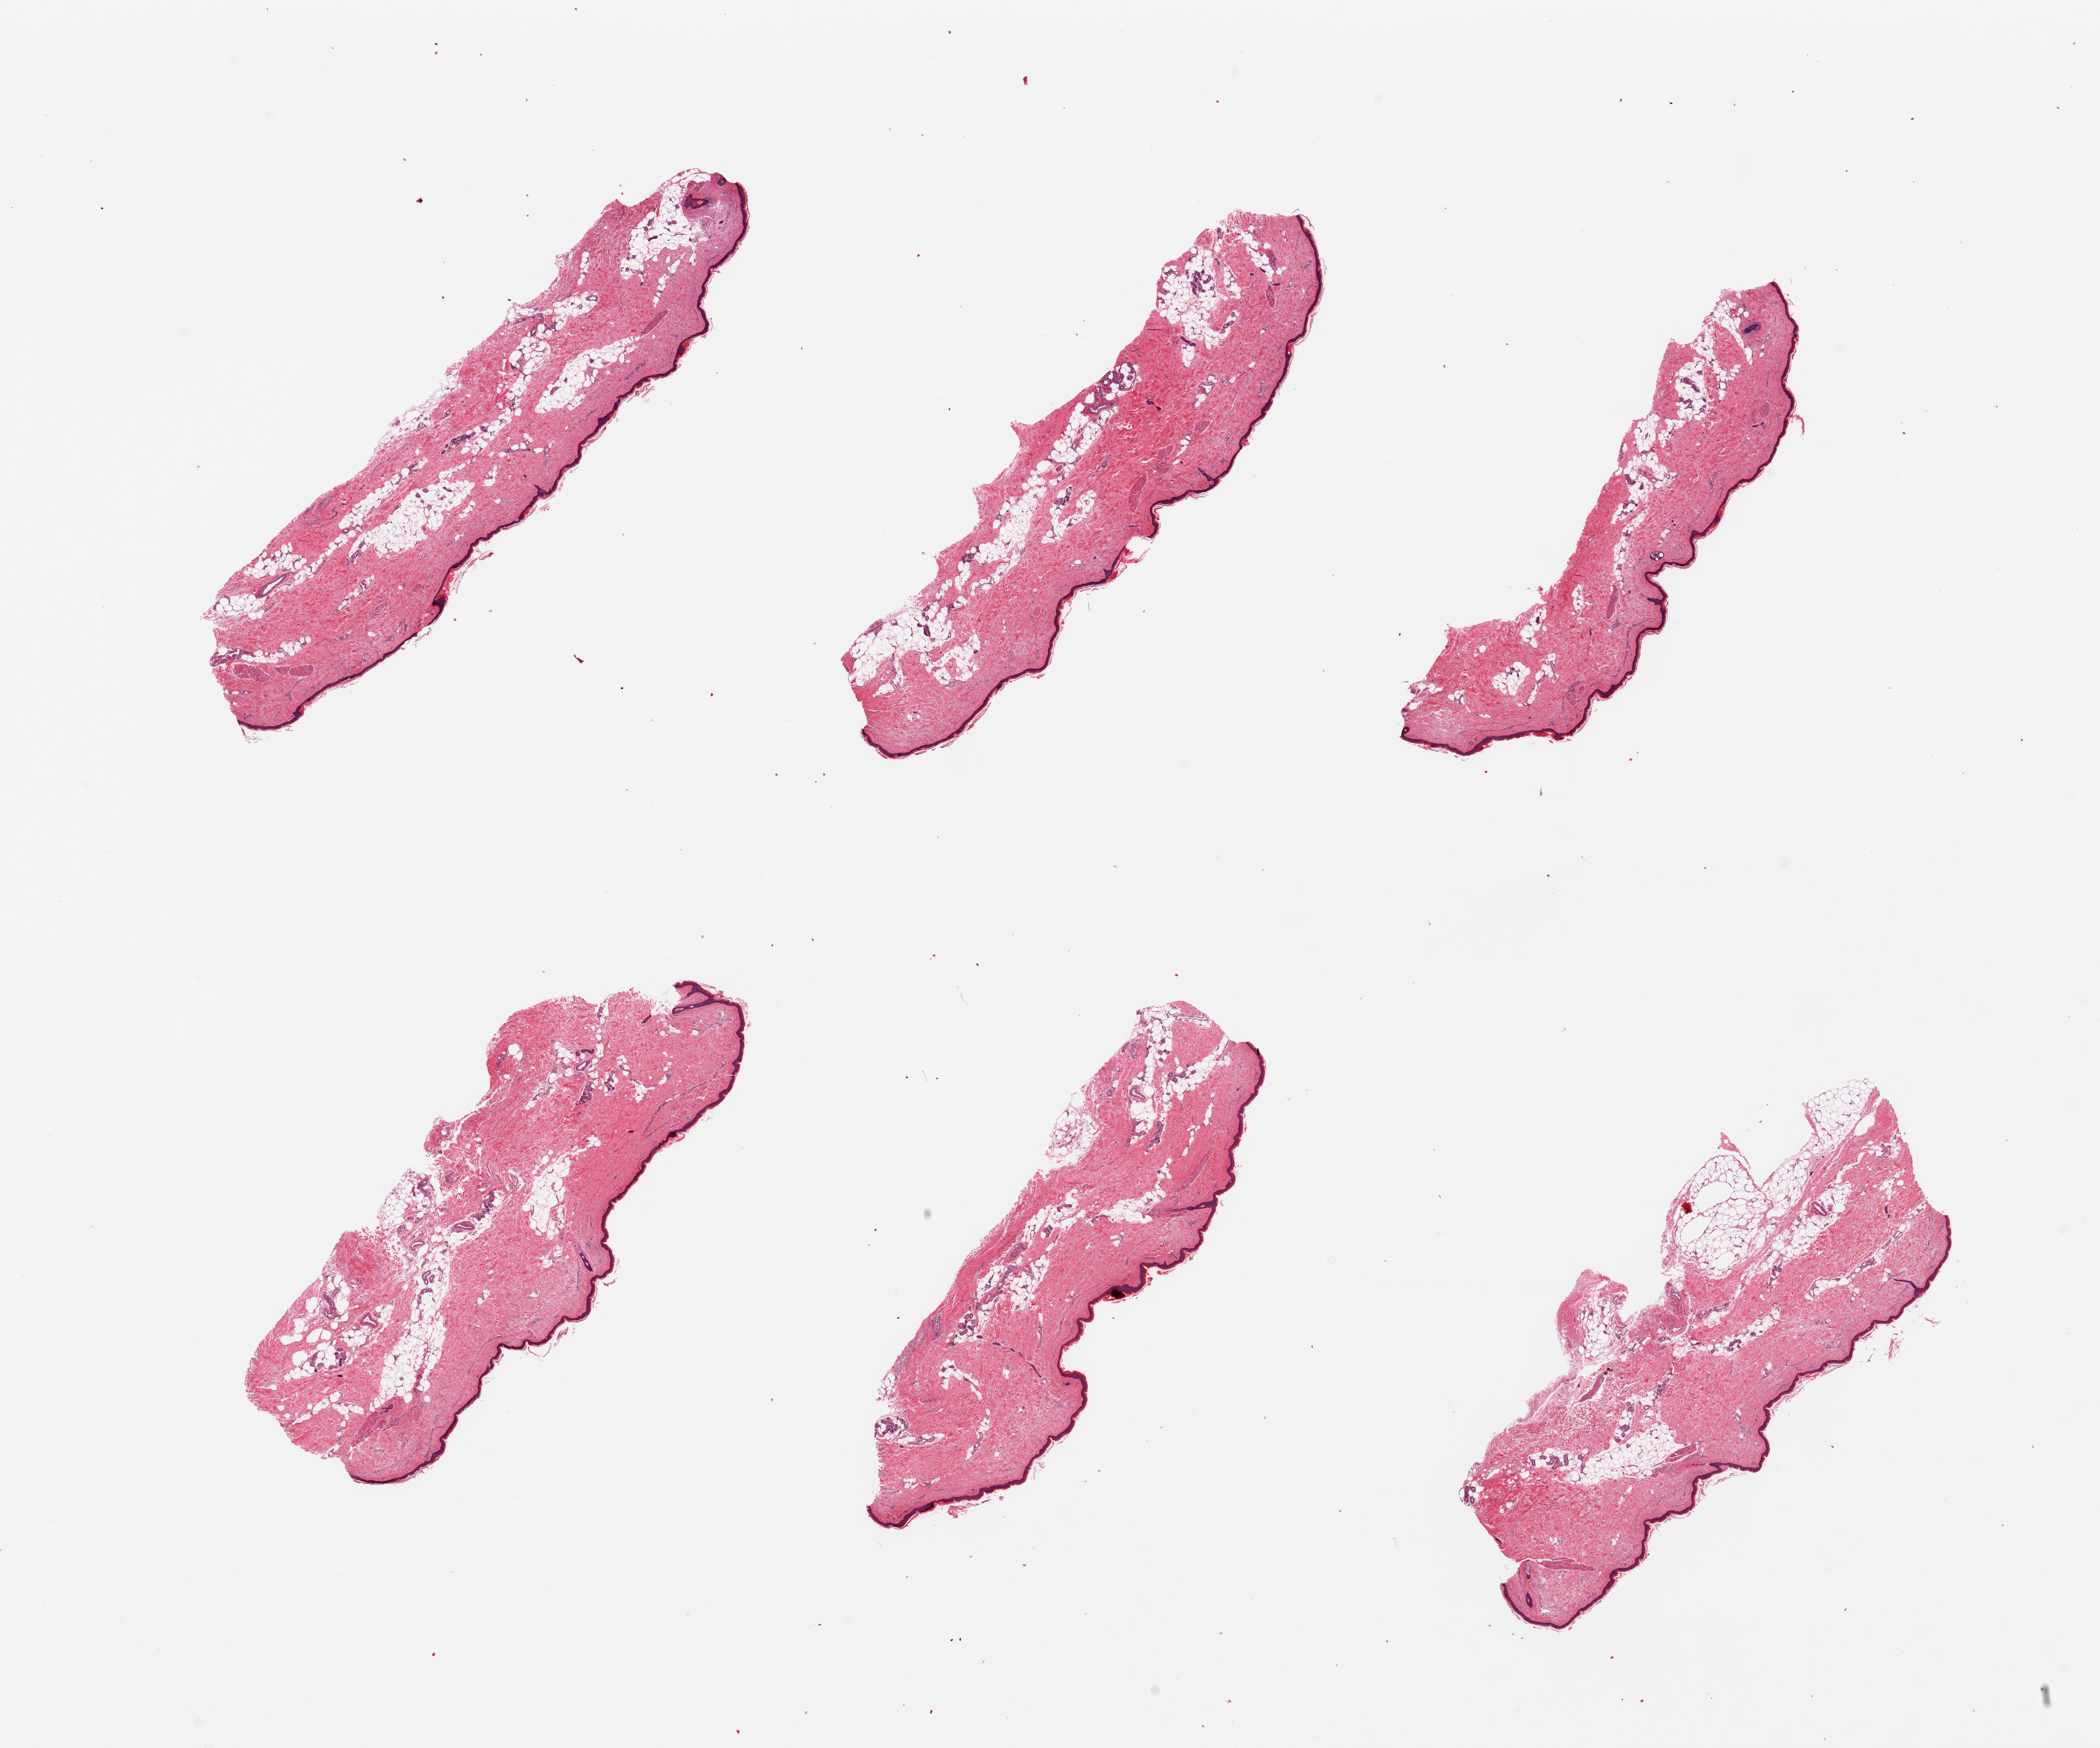
Digitized haematoxylin and eosin-stained section — low-resolution overview of the scanned area, about 24.6 x 20.5 mm (slide scanned at 20x); PAXgene-fixed, paraffin-embedded tissue; target tissue: skin of lower leg; tissue donor sample. Donor sex: female.
Pathologist's review note for this sample: 6 pieces; up to 40% internal fat.